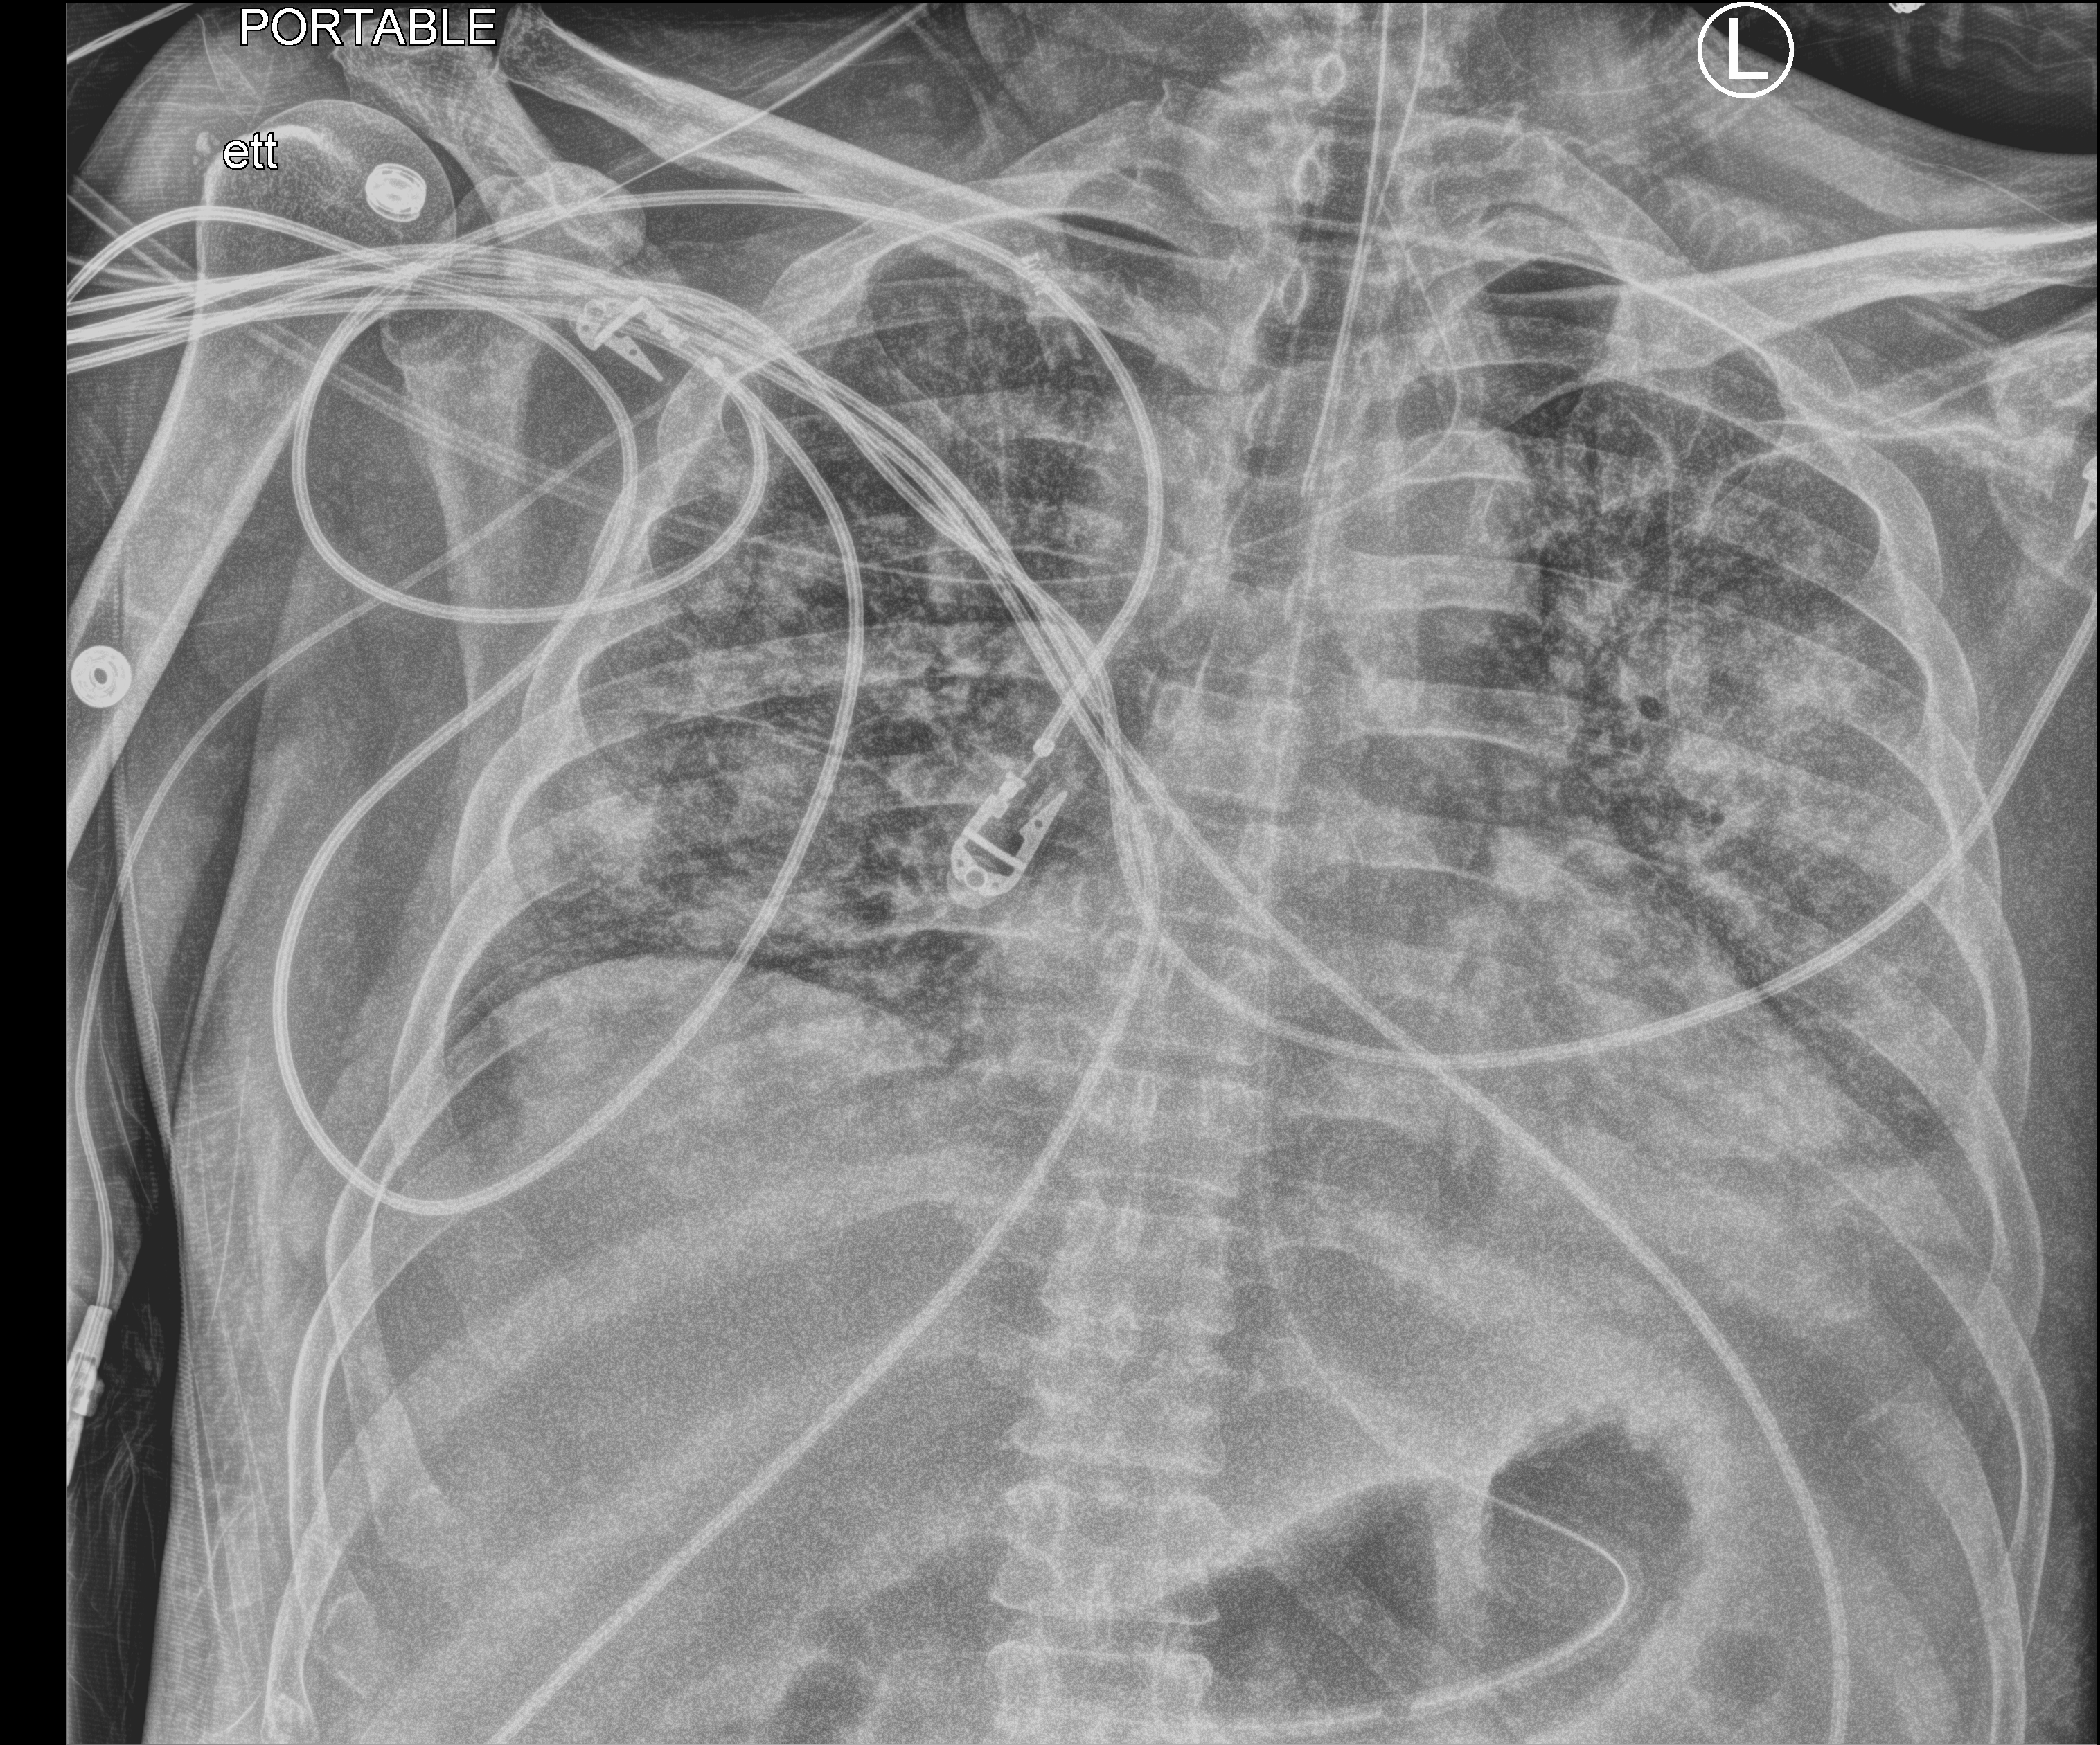
Chest X-ray (portable), anteroposterior (AP) projection. Male patient hospitalised with COVID-19, age 18–59 years.
From the hospital-stay record, not from the radiograph (when in the stay this image was taken is not recorded): length of hospital stay: 40 days; other chronic lung disease (admission record): no.